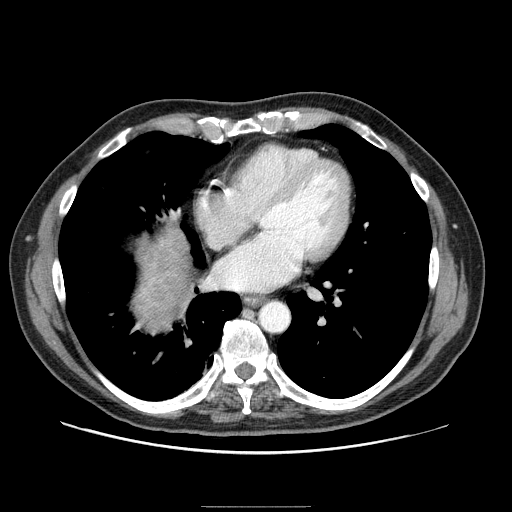
Contrast-enhanced abdominal CT (liver protocol), one axial slice. Position 89 of 99 along the scan axis. 100 kVp. One of 2 acquisitions stored at this slice position. Soft-tissue window (W 400 / L 40 HU). 512 × 512 image matrix. From the clinical record (not read from this slice): diagnosis: hepatocellular carcinoma (patient treated with transarterial chemoembolisation; whether this scan precedes or follows treatment is not stated here); TNM stage (as recorded): Stage-II; Child-Pugh class: A; tumour differentiation: well differentiated; tumour nodularity: multinodular.
Structures marked on this image (semi-automatically segmented with operator editing):
- liver parenchyma outside the tumour (the mass and vessels are separate outlines, so this box may not span the whole liver): bounding box (x1, y1, x2, y2) in pixels: (134, 226, 190, 330)